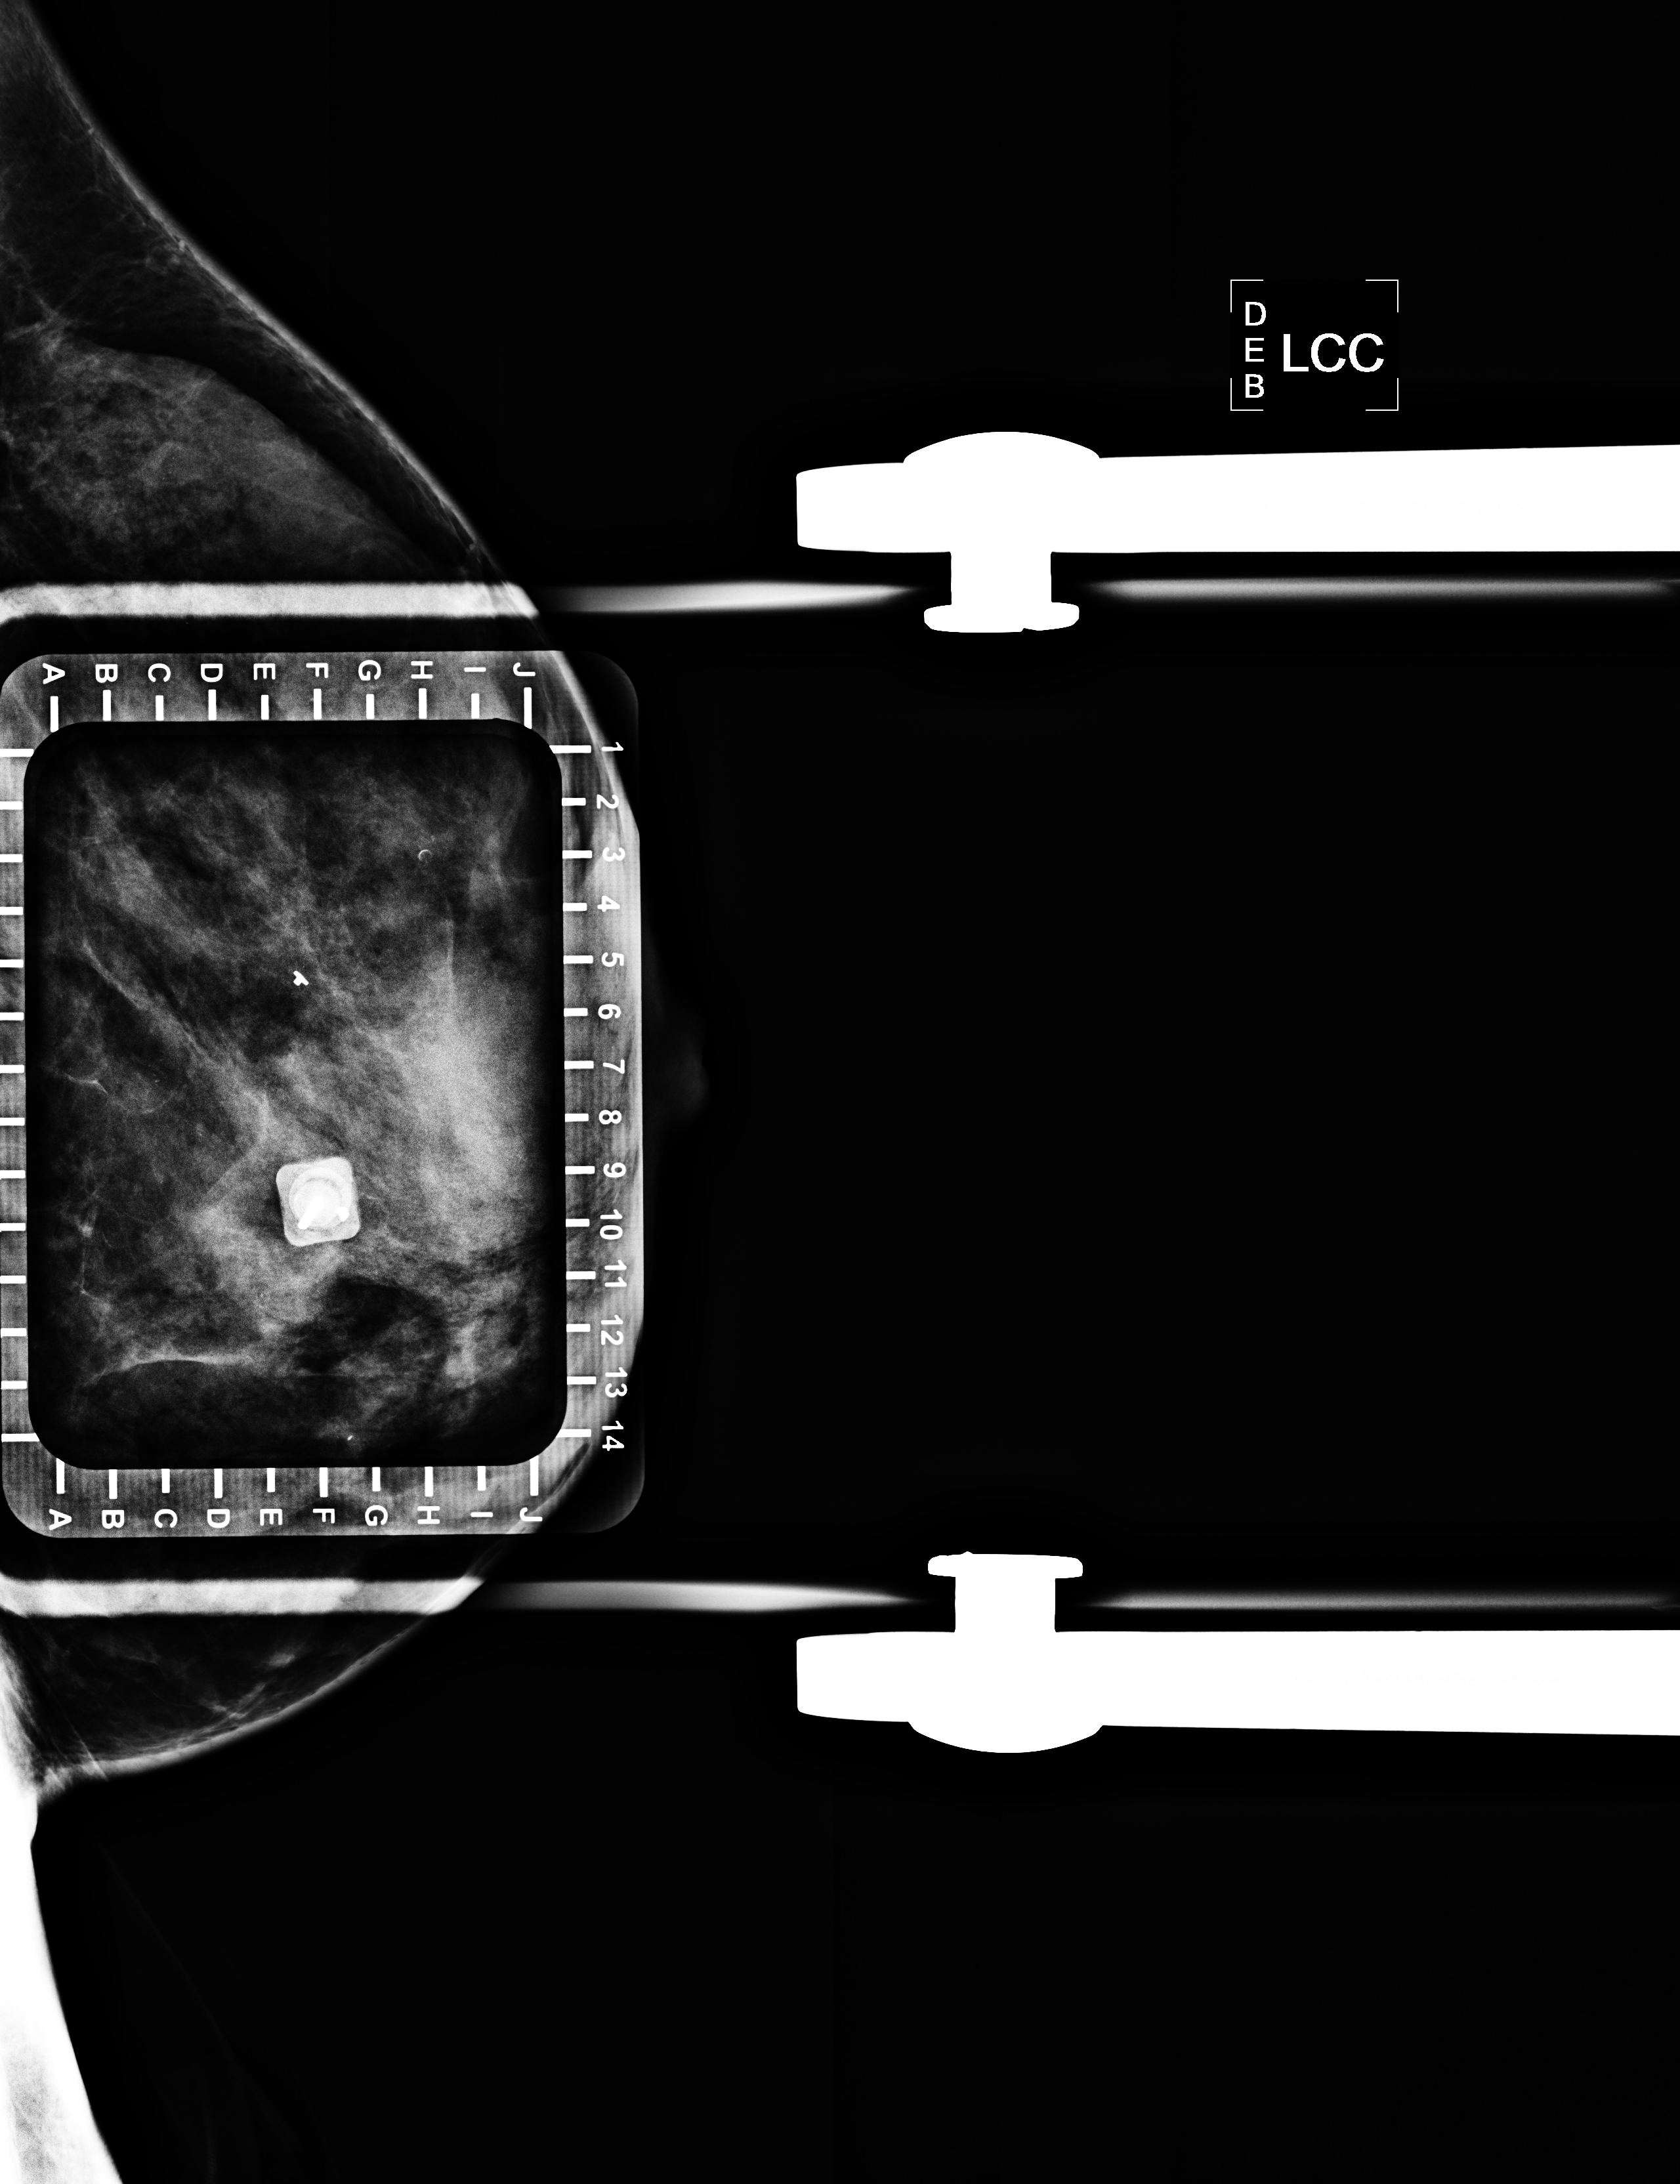
Needle-localisation mammographic view, left breast, CC view.
Patient-level pathology facts (clinical record, not image findings): pathology diagnosis: ducta CA in situ (left breast); receptor status (as recorded): ER neg, PR neg, HER2 pos.